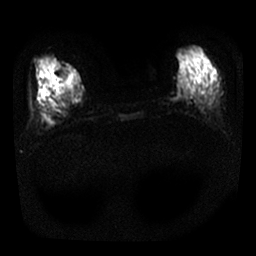
Breast MRI, one axial slice. Position 9 of 24 along the scan axis. Diffusion-weighted series; image 2 of 4 stored at this slice position (different b-values; order by instance number). 1.5 T. 256 × 256 image matrix. Female patient.
Annotated regions visible in this slice (outlined manually by an expert reader):
- tumour on diffusion-weighted imaging: box from (x=173, y=88) to (x=180, y=101) px